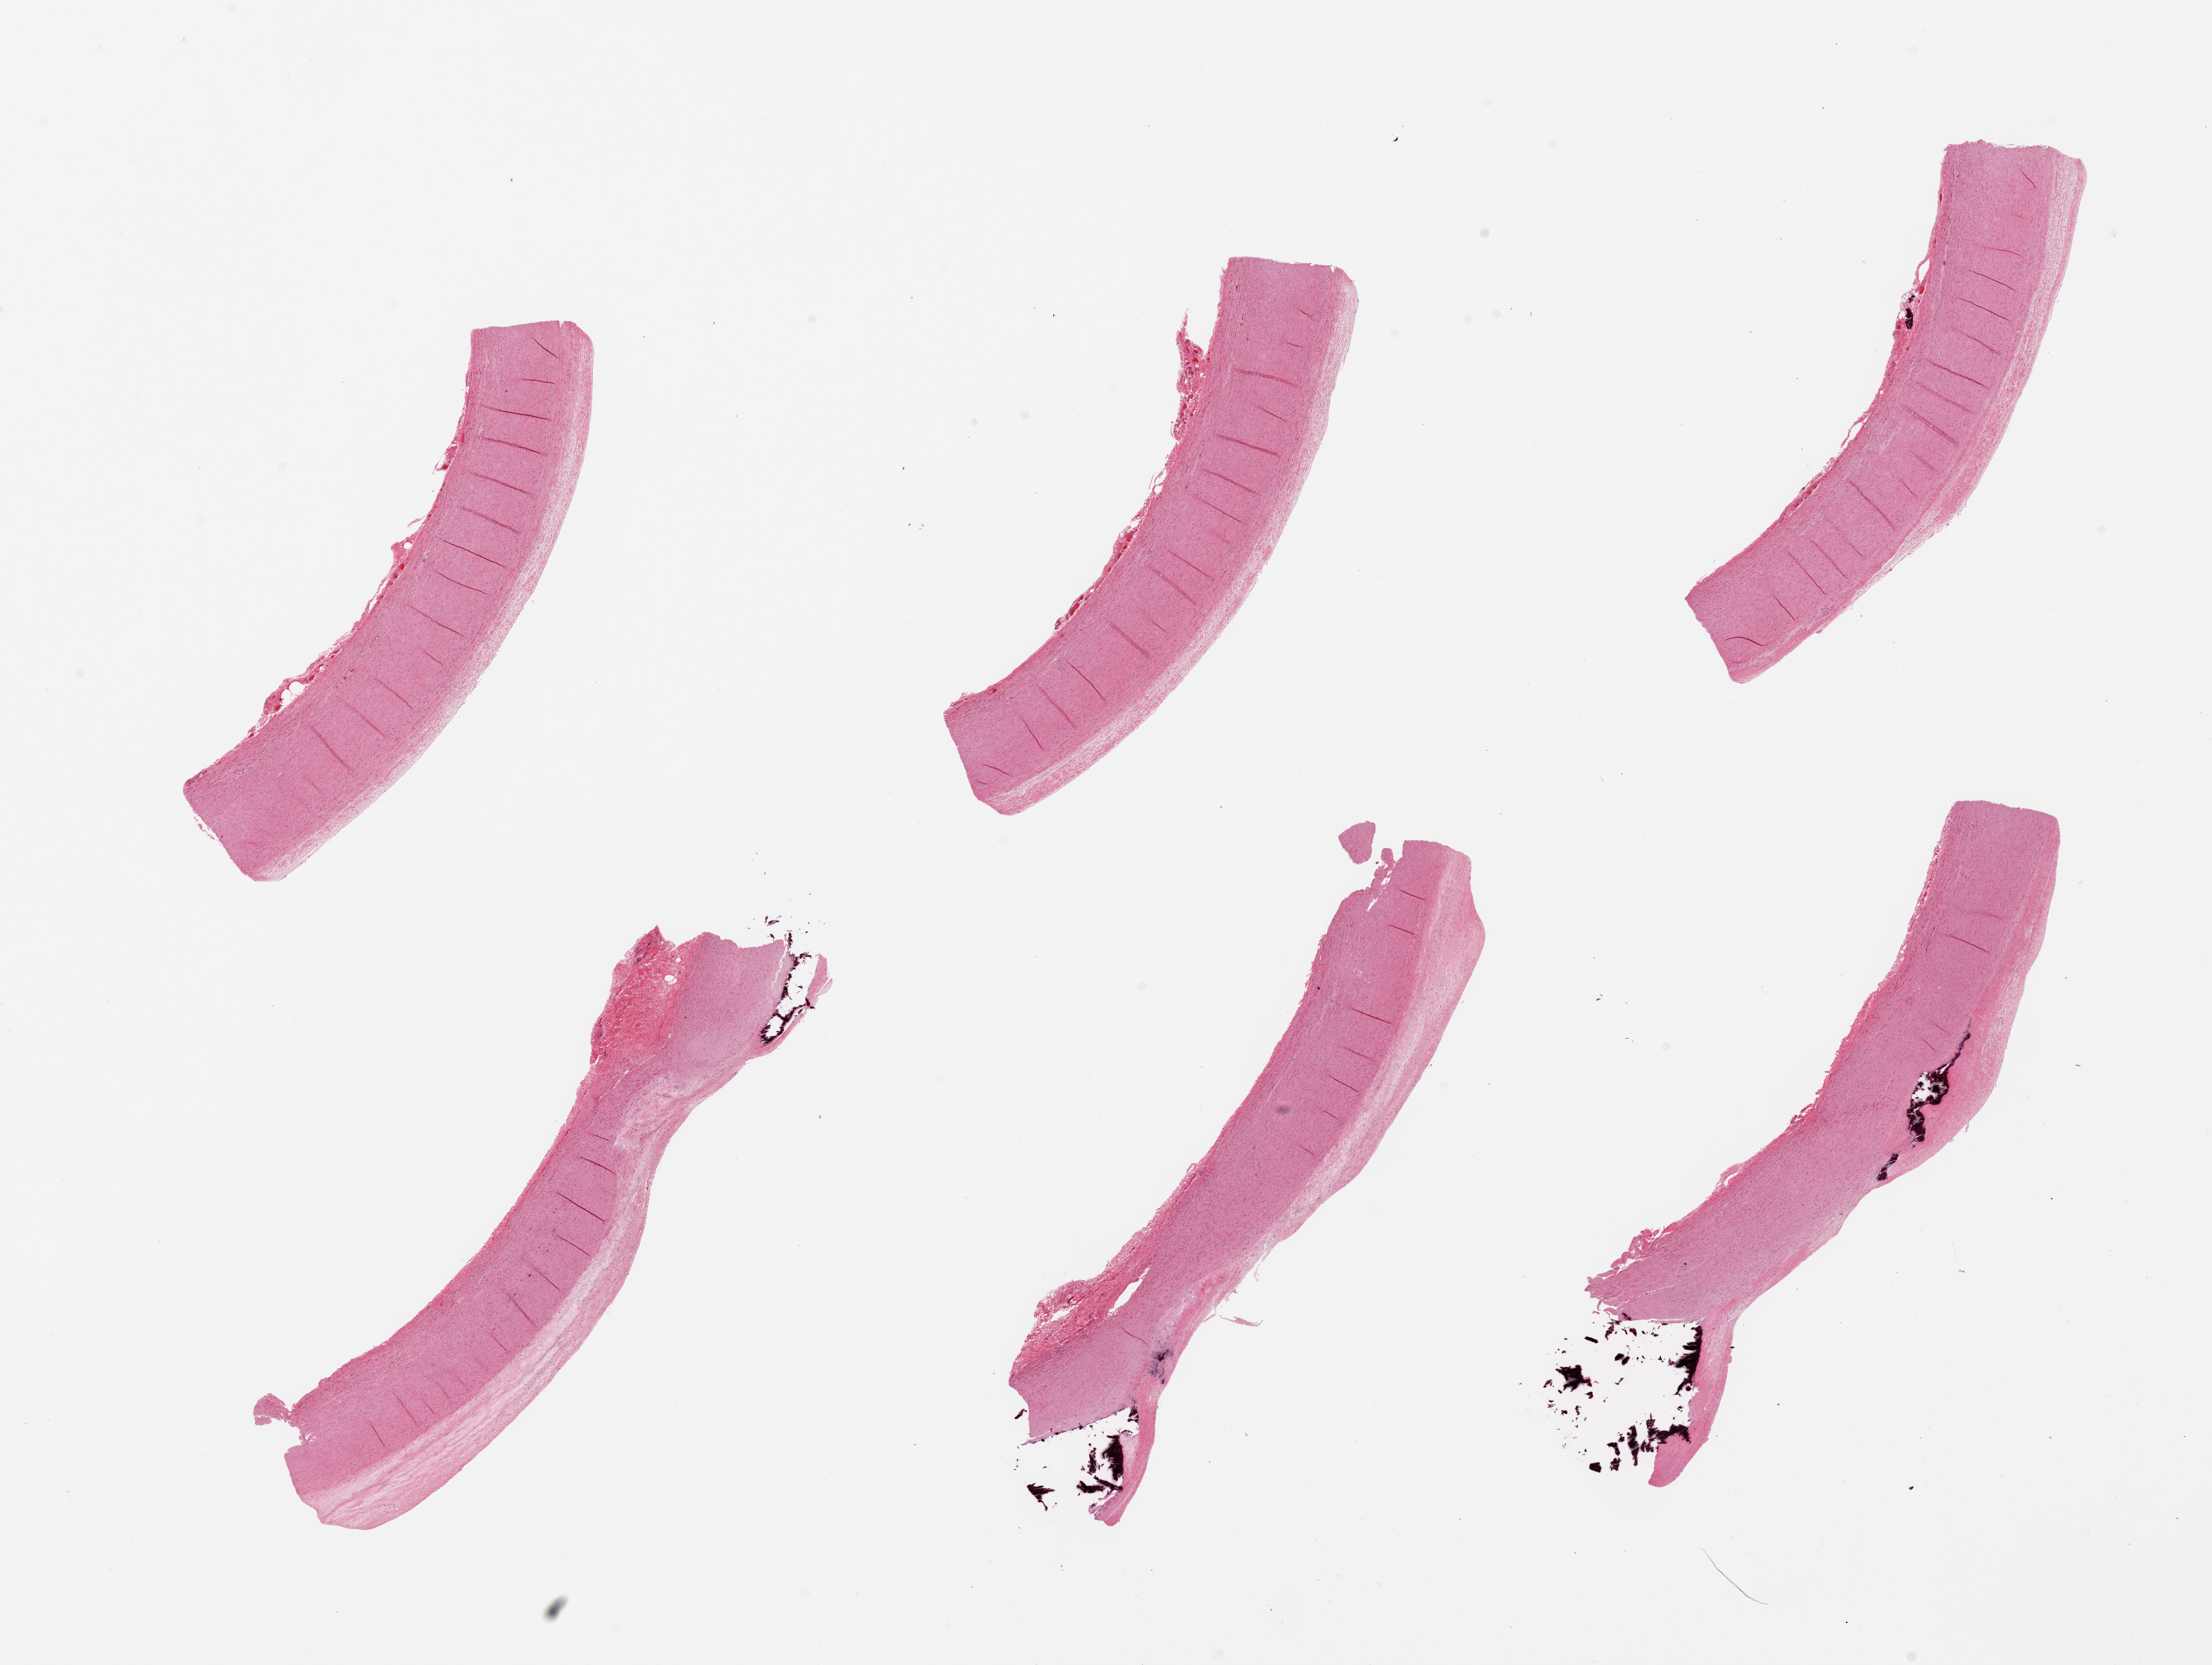
Whole-slide image, haematoxylin and eosin stain — a low-resolution overview of the entire scanned area, about 24.6 x 18.5 mm (acquisition: 20x scan); PAXgene-fixed paraffin-embedded (PFPE) section; target tissue: aorta; donor tissue sample. Male donor.
Reviewer comment on this tissue sample: 6 pieces, calcific atherosclerosis.